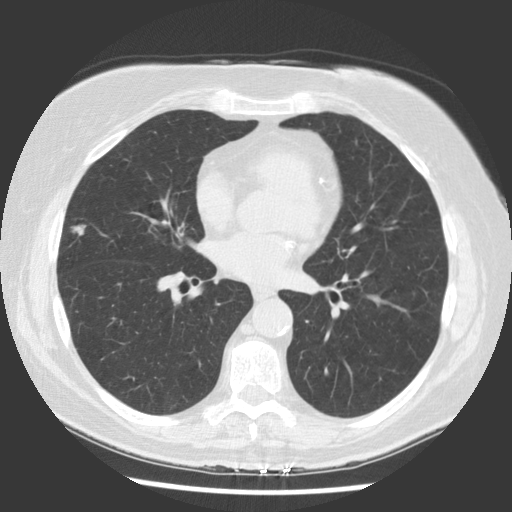
Low-dose screening chest CT, one axial slice; position 76 of 142 along the scan axis; 140 kVp; lung window (W 1500 / L -600 HU); 2.5 mm slice thickness; 512 × 512 image matrix, field of view 340 × 340 mm.
Outlined on this slice (outlined manually by an expert reader):
- lesion 1 (tumor, middle lobe of right lung): bounding box <71,225,86,236> (left, top, right, bottom; pixels)